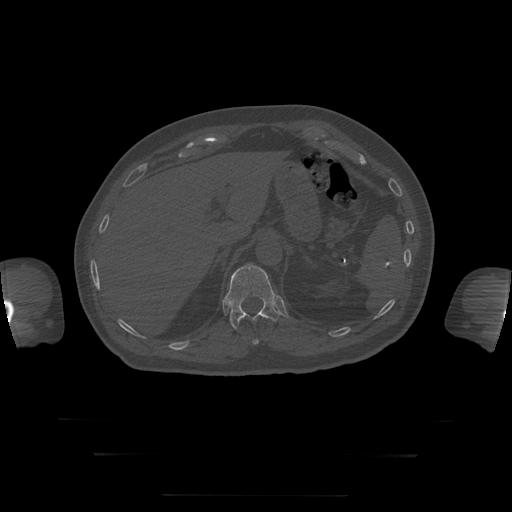
CT including the spine, one axial slice; position 80 of 397 along the scan axis; 120 kVp; bone window (W 1800 / L 400 HU); 1.25 mm slice thickness; 512 × 512 image matrix. Patient age 73 years. From the clinical record (not read from this slice): primary cancer: prostate.
Outlined on this slice (semi-automatically segmented with operator editing):
- T11 vertebra: box from (x=252, y=340) to (x=259, y=345) px
- T12 vertebra: (x=227, y=265)–(x=281, y=330)